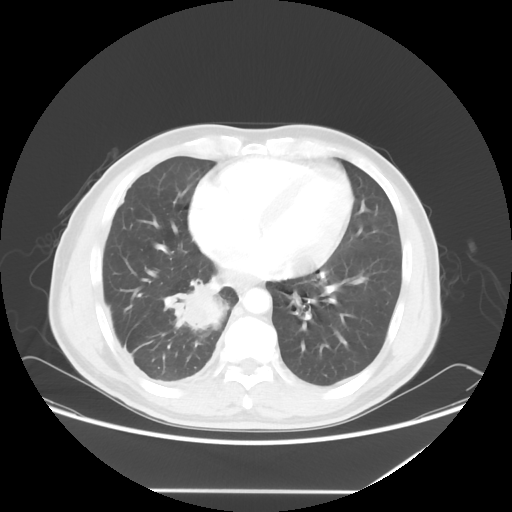
Chest CT, one axial slice. Position 22 of 60 along the scan axis. Reconstruction kernel STANDARD. 120 kVp. Lung window (W 1500 / L -600 HU). 5 mm slice thickness. 512 × 512 image matrix, field of view 419 × 419 mm. Patient: male, 48 years. From the clinical record (not read from this slice): clinical TNM (as recorded): T3 N3 M1a.
Outlined on this slice (rectangle marked by the reading radiologist):
- lung tumour (recorded histology: squamous cell carcinoma): box from (x=164, y=279) to (x=235, y=339) px